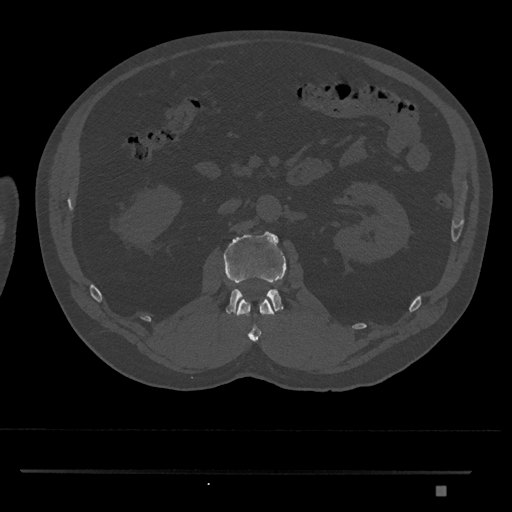
CT including the spine, one axial slice; position 782 of 1134 along the scan axis; reconstruction kernel Br40s/3; bone window (W 1800 / L 400 HU); 0.5 mm slice thickness; 512 × 512 image matrix, field of view 429 × 429 mm. Male patient, age 65 years. Case-level facts recorded for this patient, not image findings: primary cancer: prostate.
Outlined on this slice (semi-automatically segmented with operator editing):
- L1 vertebra: box from (x=236, y=297) to (x=275, y=342) px
- L2 vertebra: (x=223, y=231)–(x=287, y=316)